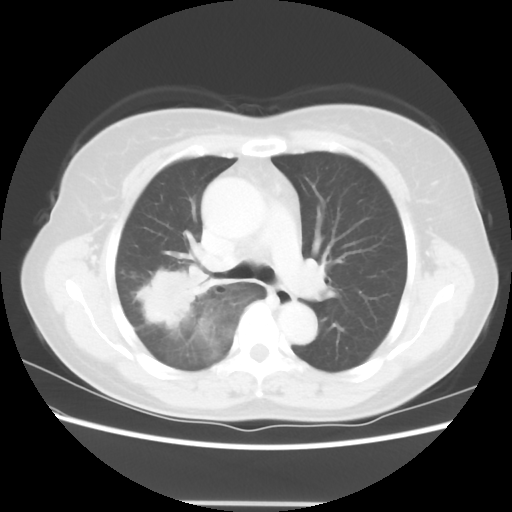
Chest CT, one axial slice; slice 38 of 56 in the series (ordered by position); lung window (W 1500 / L -600 HU); 5 mm slice thickness; 512 × 512 image matrix, field of view 360 × 360 mm. Patient: female, 55 years. Case-level facts recorded for this patient, not image findings: clinical TNM (as recorded): T2 N1 M0; histopathological grade: G2-3.
Annotated regions visible in this slice (bounding box drawn by a radiologist):
- lung tumour (recorded histology: adenocarcinoma): bounding box (x1, y1, x2, y2) in pixels: (129, 250, 213, 339)